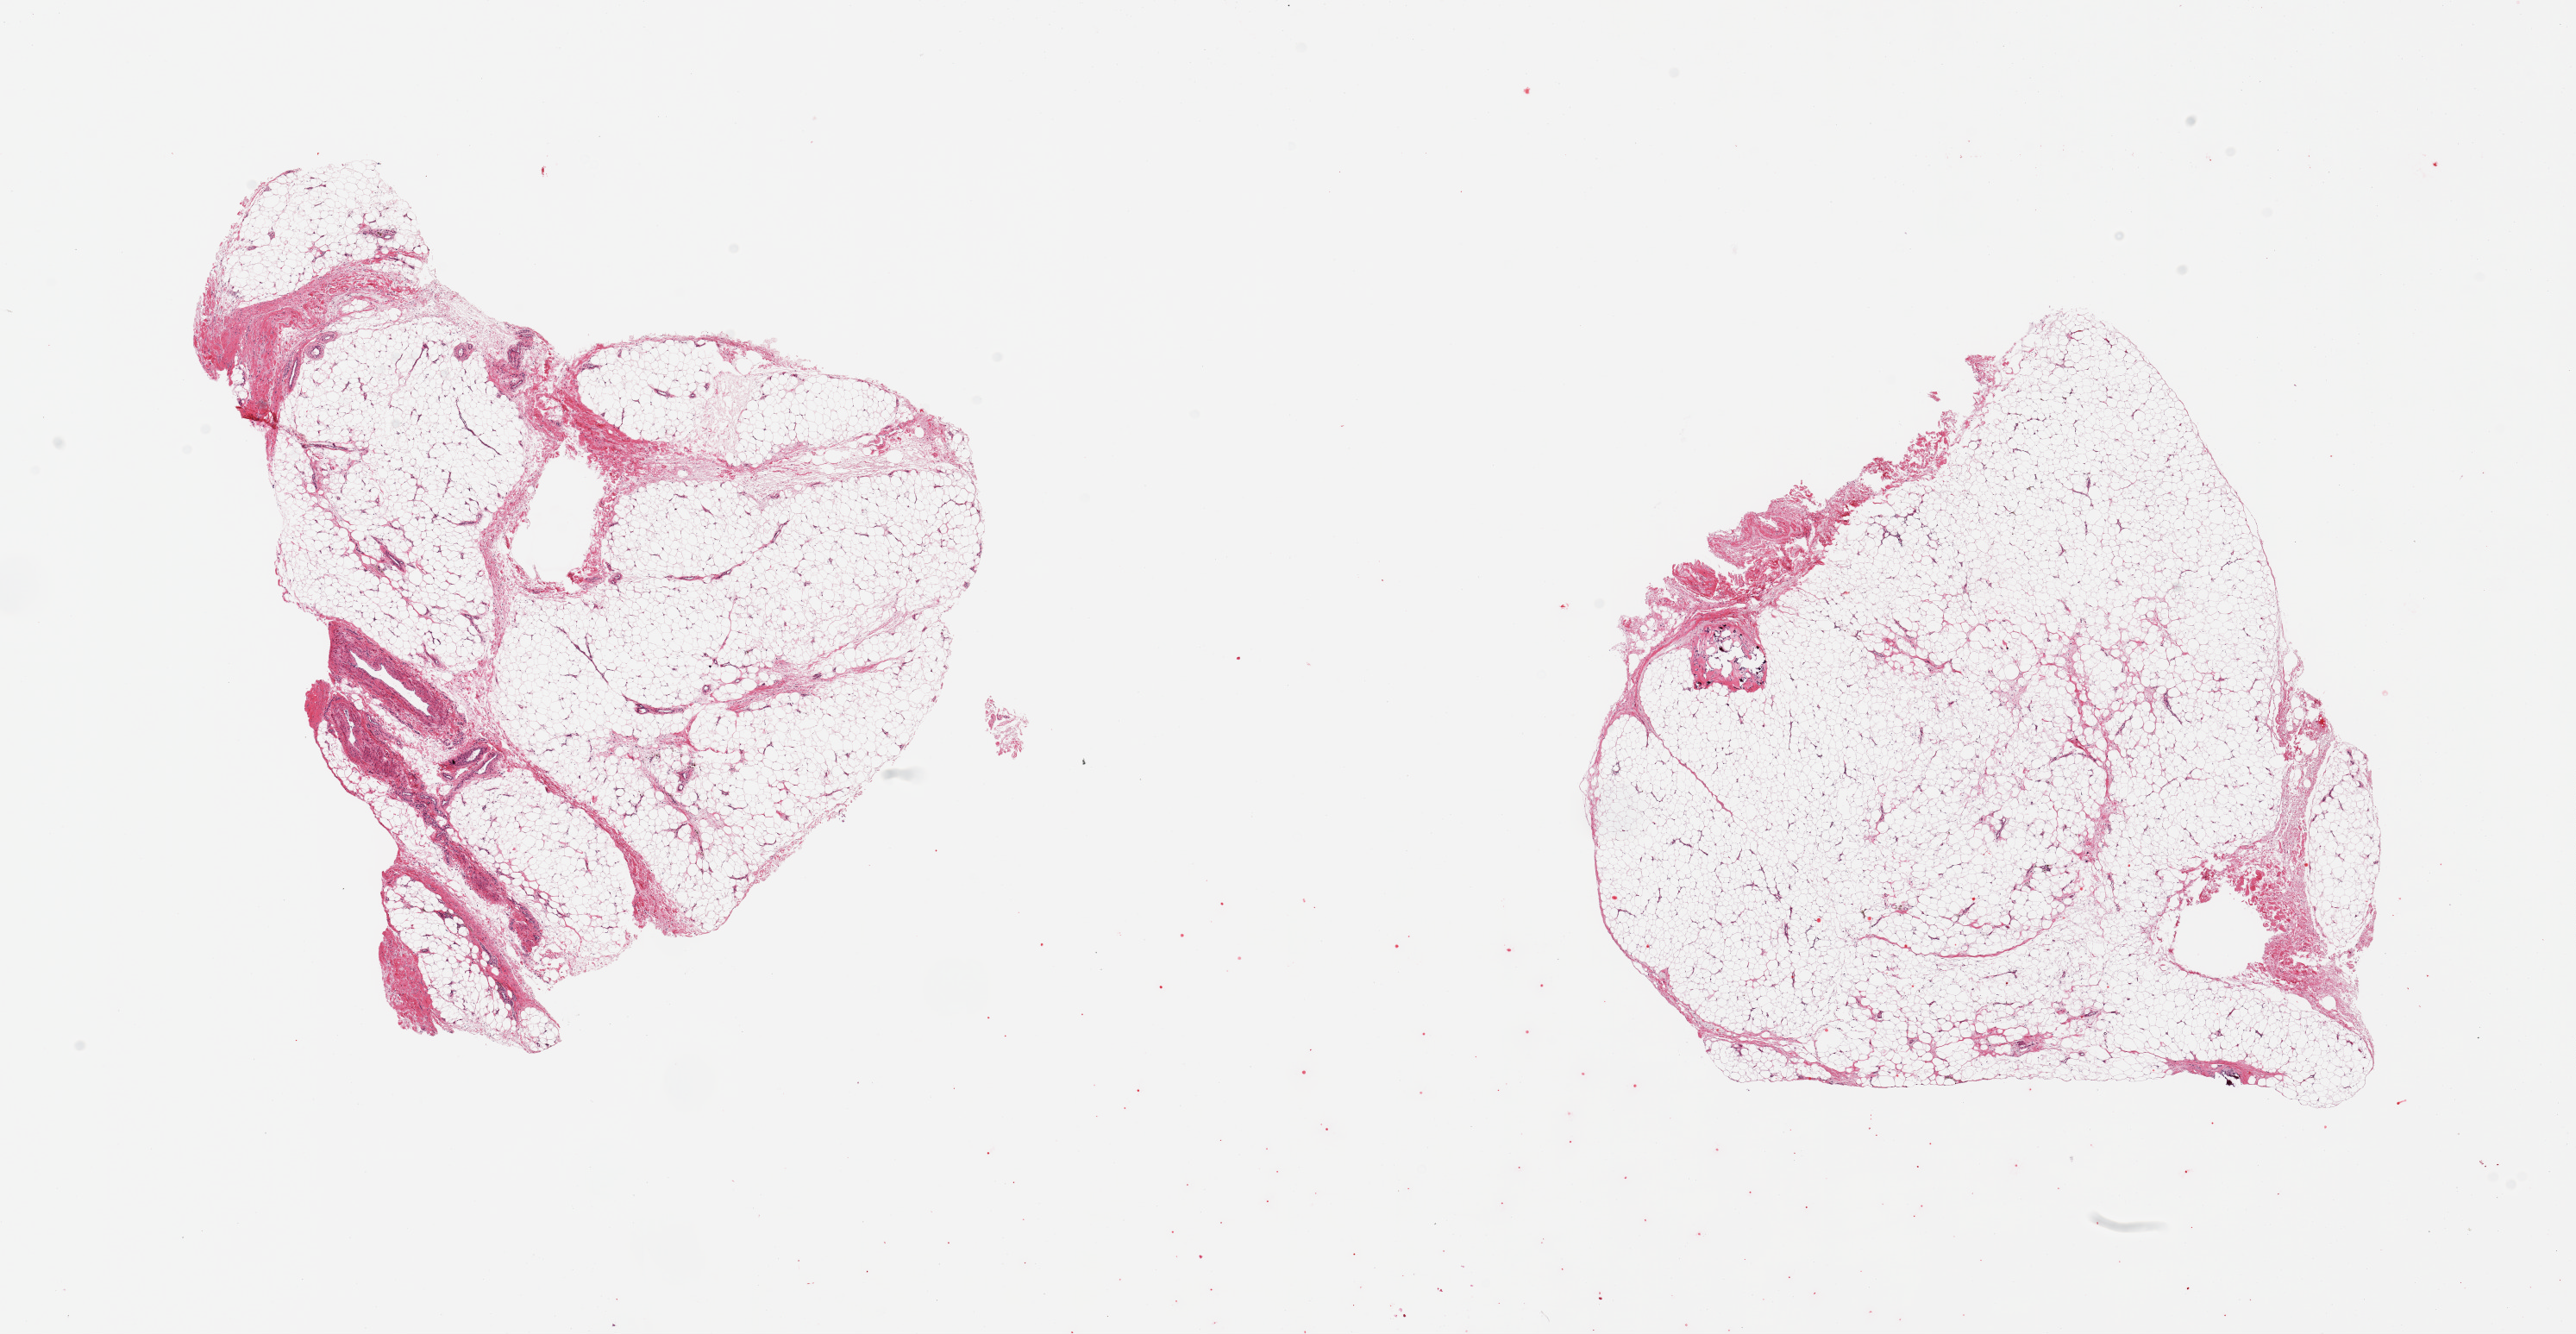
Hematoxylin and eosin (H&E) whole-slide image, brightfield — a low-resolution overview of the entire scanned area, about 23.6 x 12.2 mm, PAXgene-fixed, paraffin-embedded tissue, sampled site (target tissue): adipose tissue, donor tissue sample. Male donor.
• pathologist's review note for this sample: 2 pieces; focus of dystrophic calcification; 10% fibrous content